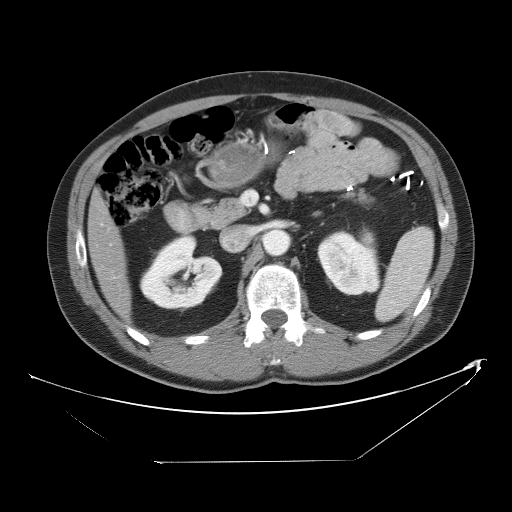
Contrast-enhanced abdominal CT, one axial slice; position 24 of 53 along the scan axis; reconstruction kernel STANDARD; 120 kVp; intravenous contrast given; soft-tissue window (W 400 / L 40 HU); 512 × 512 image matrix, field of view 438 × 438 mm. Male patient, age 59 years. Case-level facts recorded for this patient, not image findings: diagnosis: colorectal cancer liver metastases, imaged before liver resection; multiple liver metastases: yes; largest metastasis: 8.5 cm; disease in both lobes: no.
Annotated regions visible in this slice (manually delineated by an expert):
- liver: box from (x=89, y=197) to (x=129, y=317) px
- planned liver remnant (the part of the liver to remain after resection): (x=89, y=198)–(x=129, y=317)